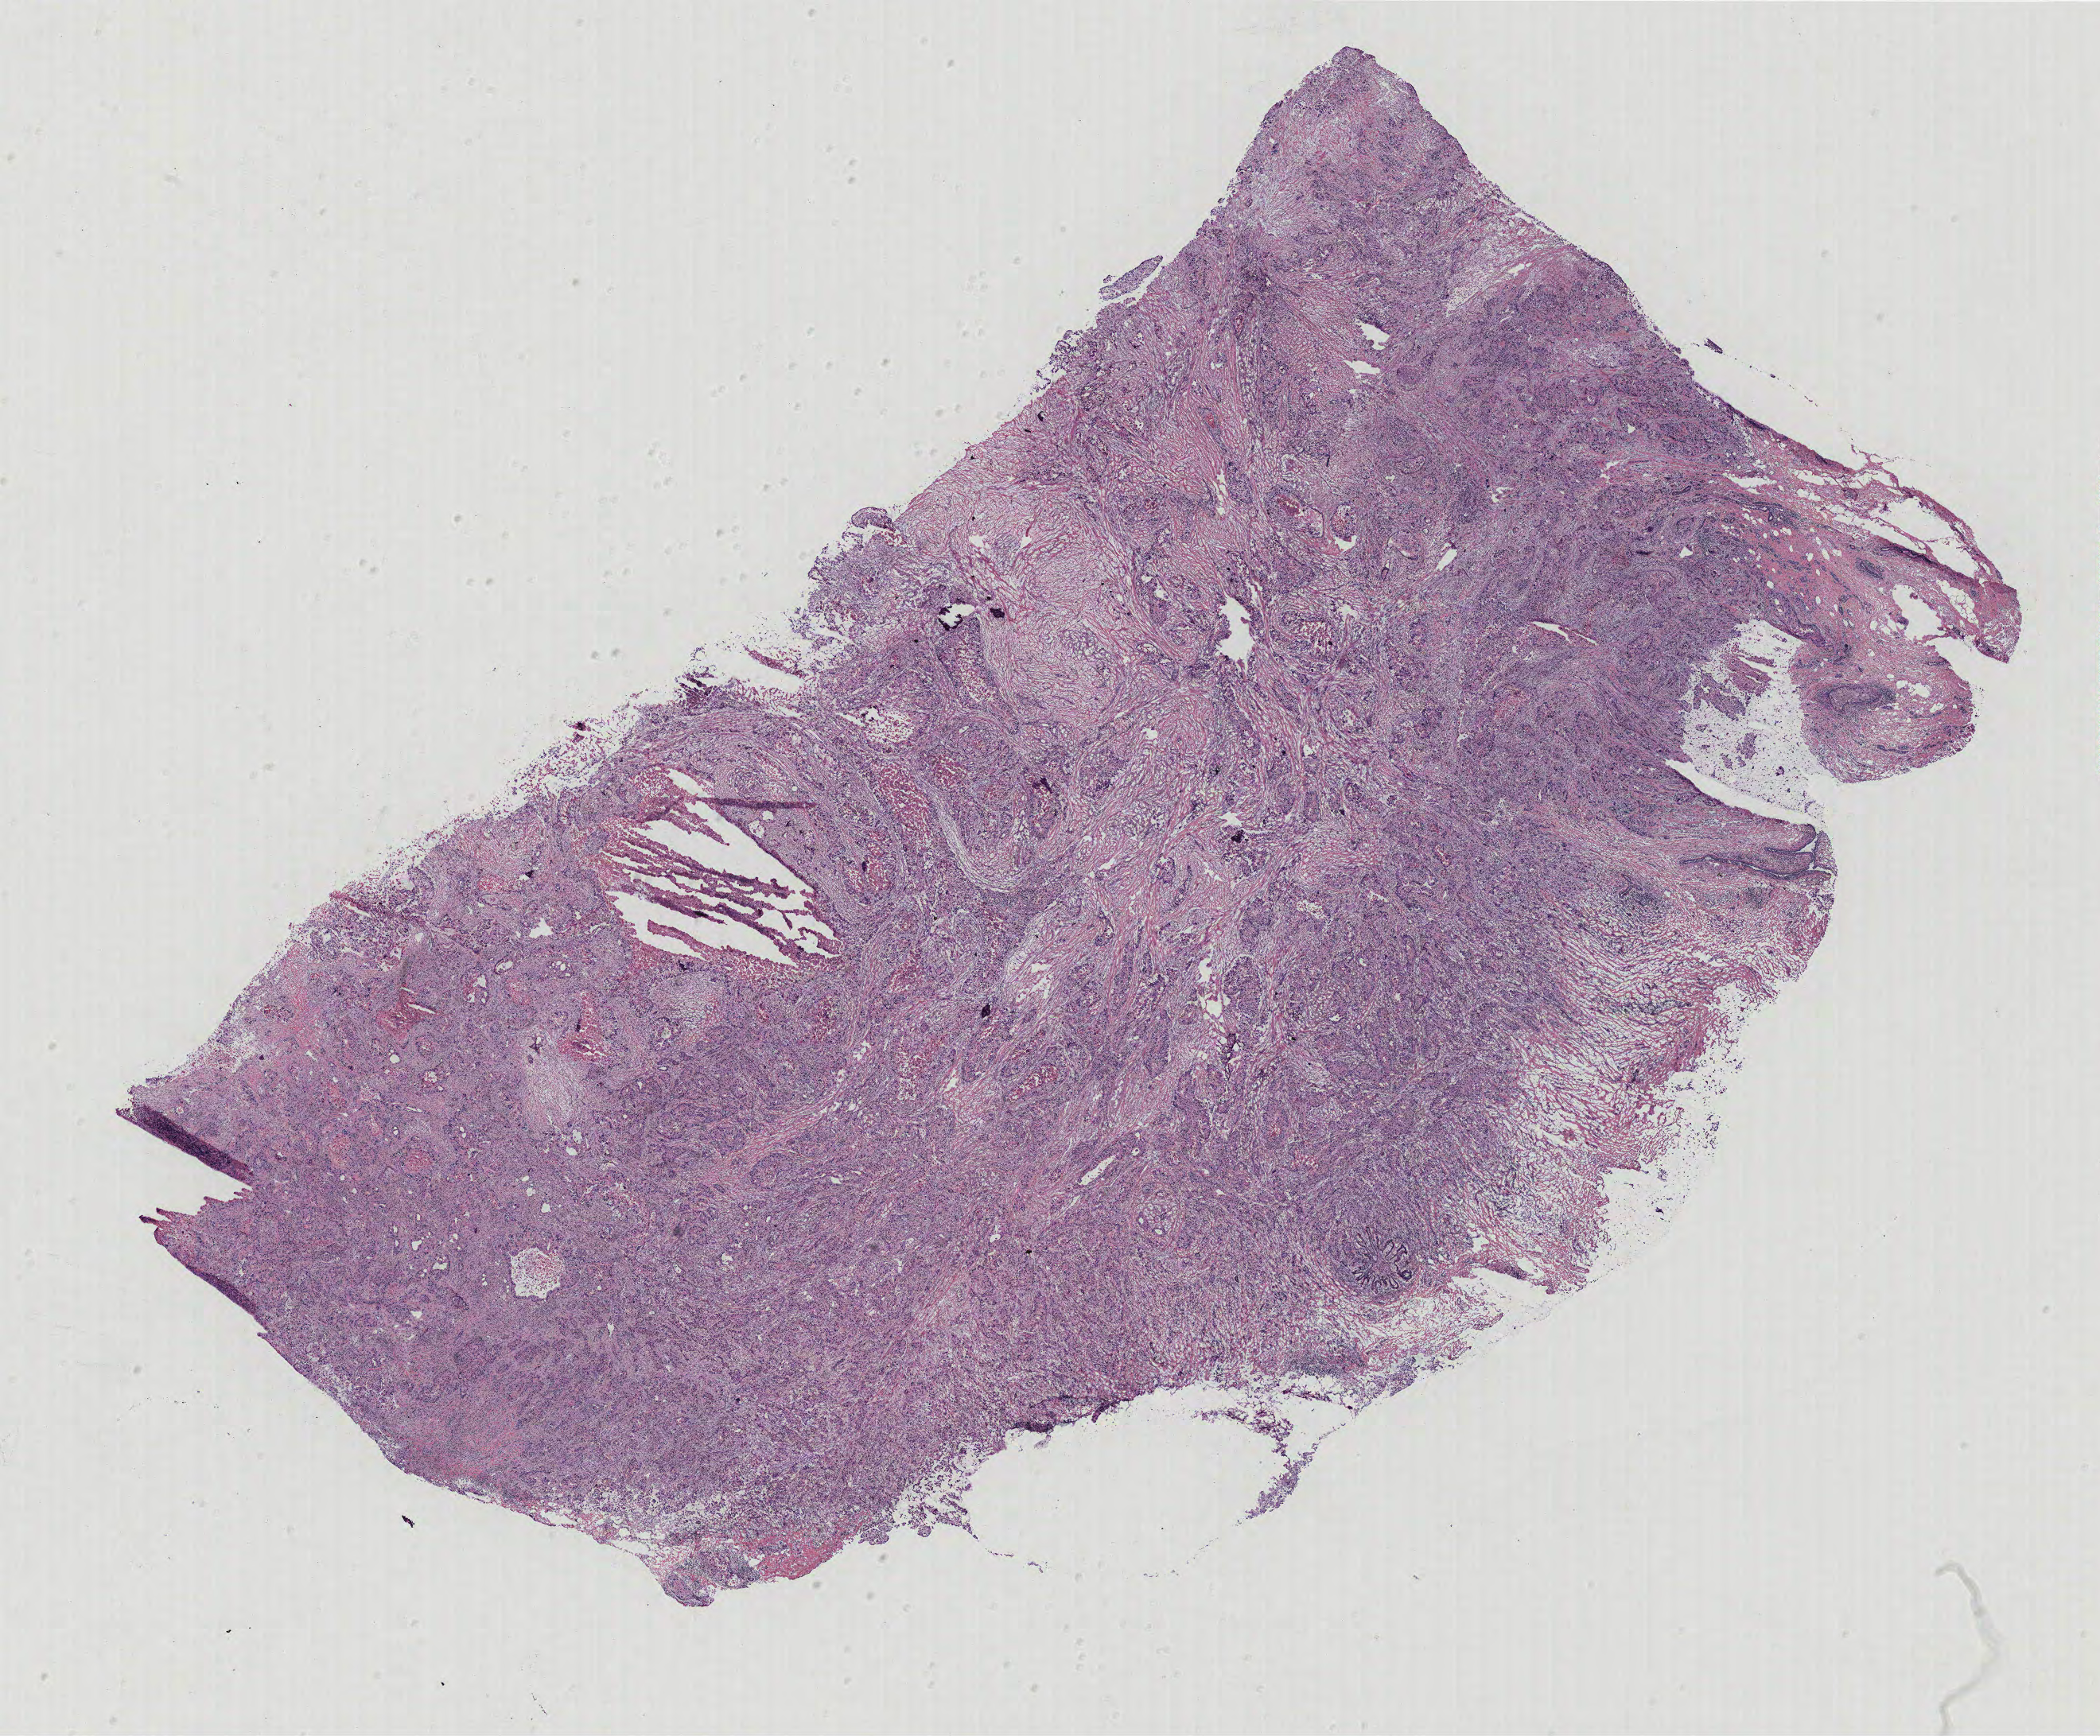
Hematoxylin and eosin (H&E) stained whole-slide image, low-resolution overview of the scanned area, about 21.1 x 17.5 mm (slide scanned at 40x). Breast, tumour tissue. Female, 71 y/o.
• AJCC pathologic stage: IIA
• diagnosis: Infiltrating duct carcinoma, NOS